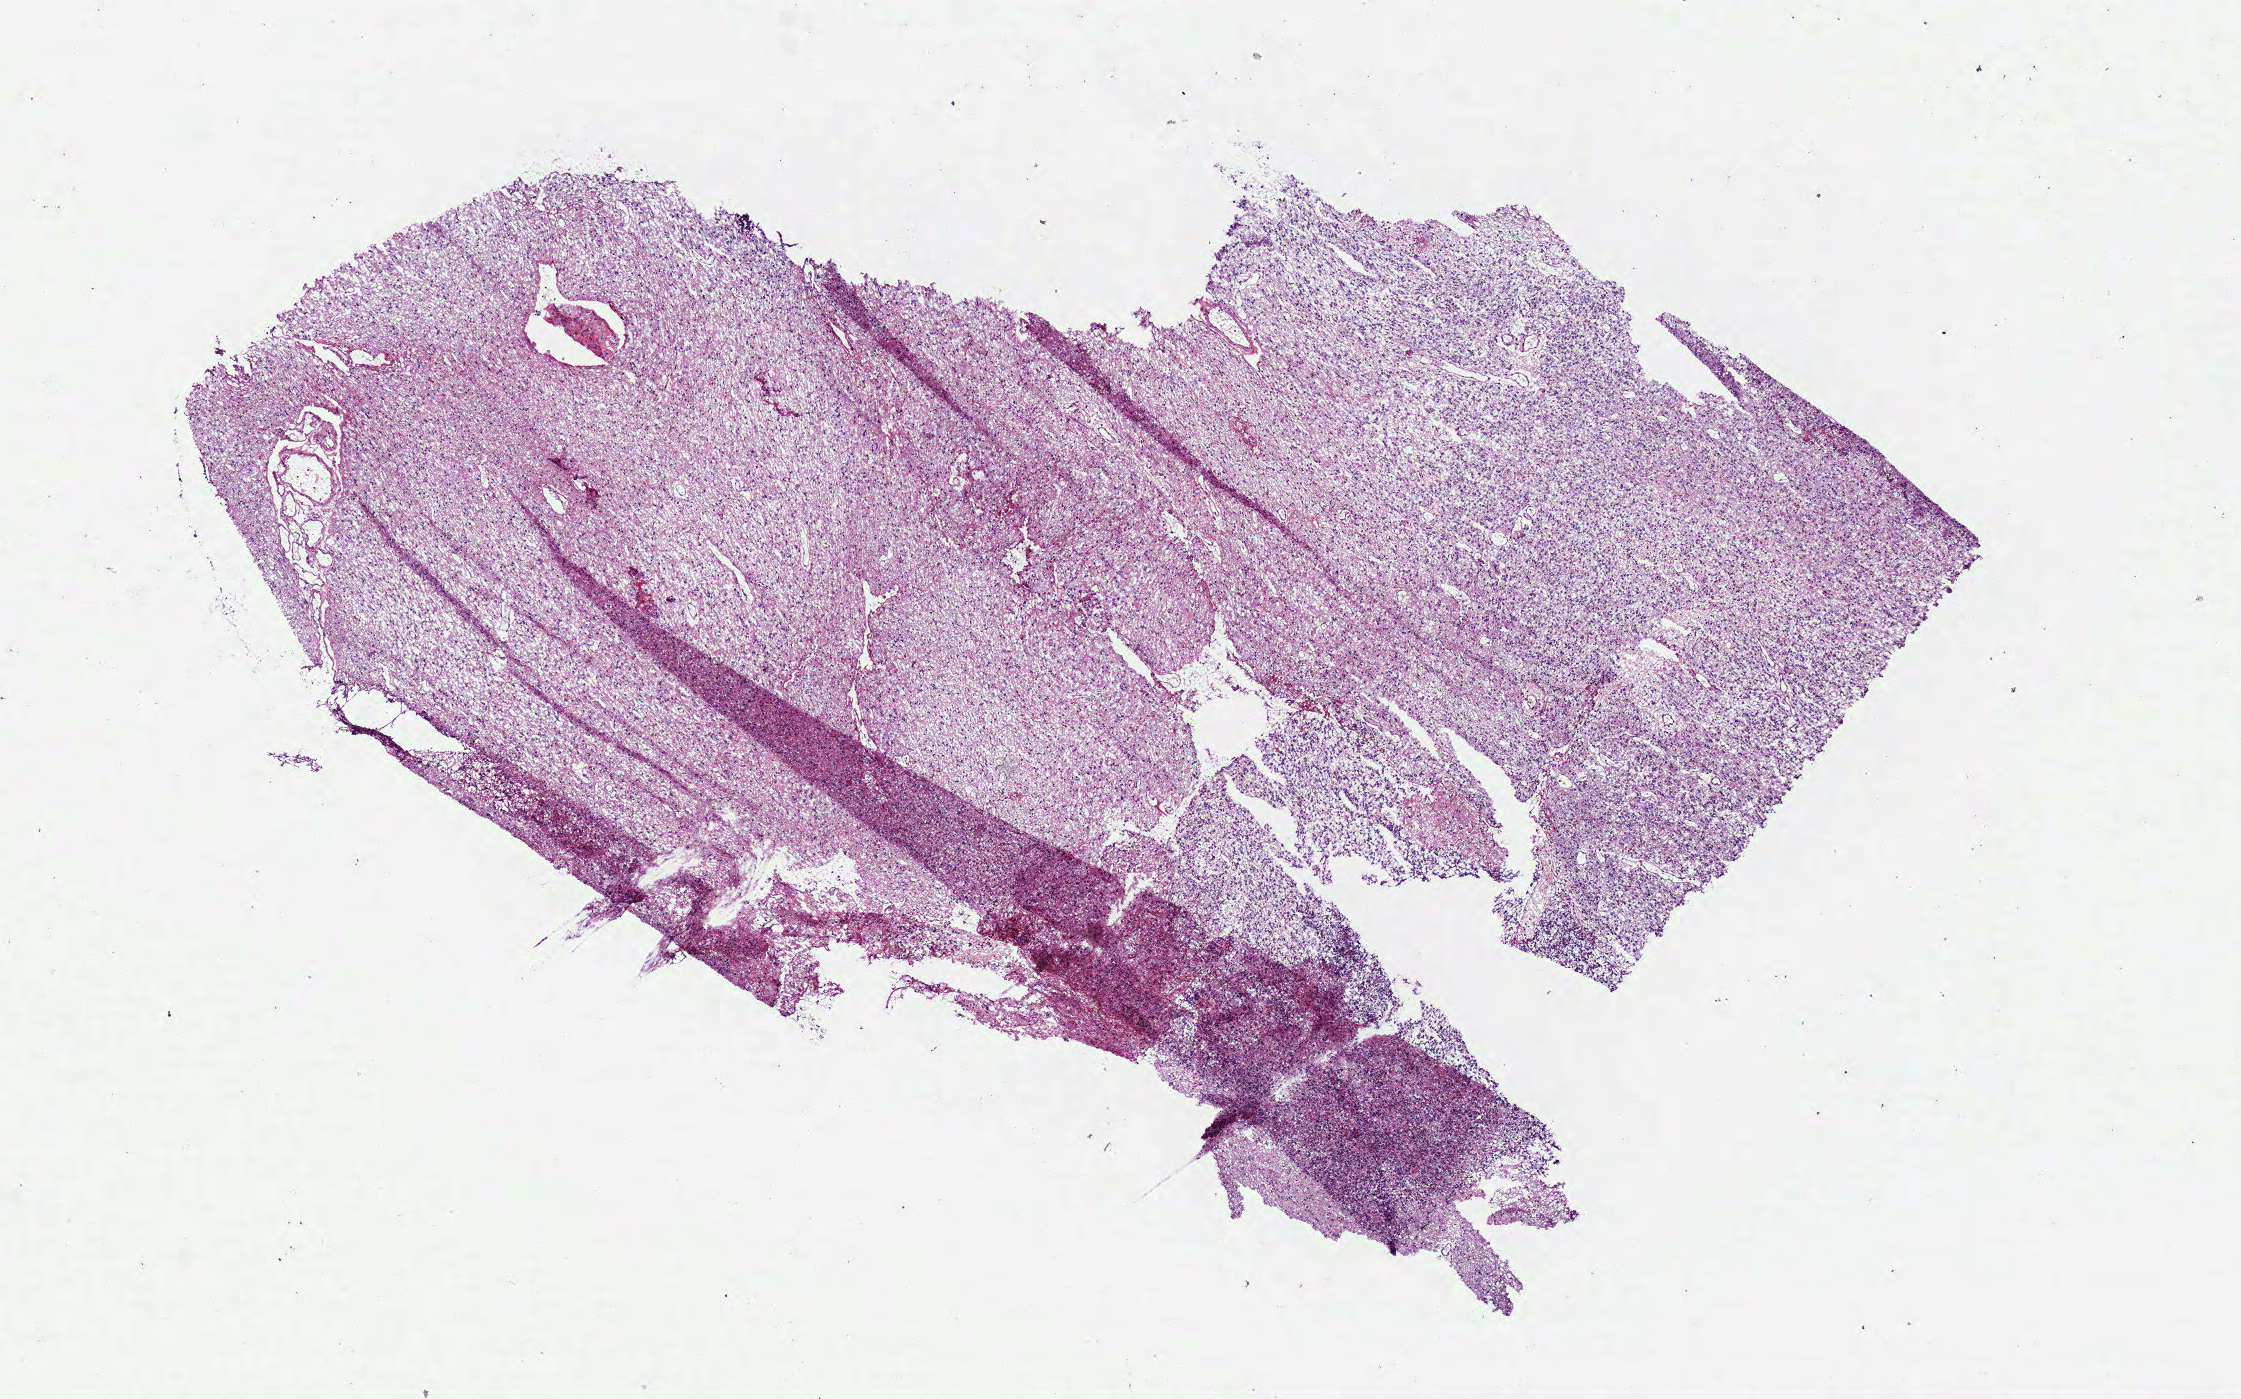
Digitized H&E tissue section (whole slide), a low-resolution overview of the entire scanned area, about 8.8 x 5.5 mm, frozen section from the bottom of the tissue portion, sample: primary tumour, brain. Patient: male, age at initial diagnosis 45 years. Histologic grade: G3 (poorly differentiated). Pathologist review of this section (percent, as recorded): tumour cells 100%, tumour nuclei 70%, normal cells 0%, stromal cells 0%, necrosis 0%.
- pathologic diagnosis: Oligodendroglioma, anaplastic